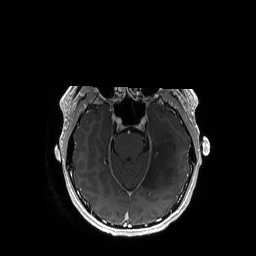
Brain MRI from a brain-tumour surgery series, one axial slice; slice 117 of 192 in the series (ordered by position); T1-weighted post-contrast; 256 × 256 image matrix, field of view 256 × 256 mm. From the clinical record (not read from this slice): histopathology: Astrocytoma; WHO grade: 3; IDH mutation: yes; tumour location: Left Temporal.
Annotated regions visible in this slice (expert manual segmentation):
- tumour: box from (x=143, y=114) to (x=178, y=190) px